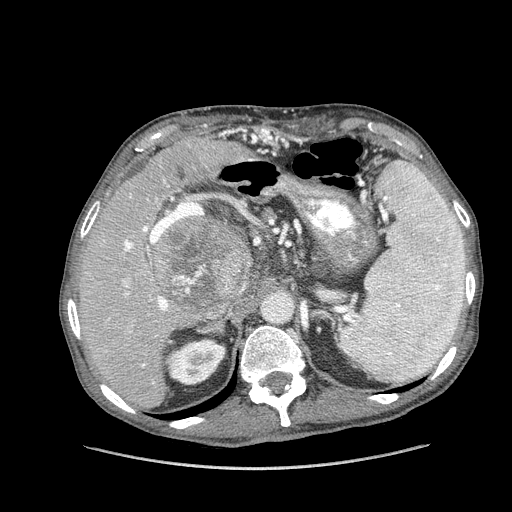
Contrast-enhanced abdominal CT (liver protocol), one axial slice; position 91 of 162 along the scan axis; reconstruction kernel STANDARD; 100 kVp; soft-tissue window (W 400 / L 40 HU); 2.5 mm slice thickness; 512 × 512 image matrix, field of view 400 × 400 mm. Case-level facts recorded for this patient, not image findings: diagnosis: hepatocellular carcinoma (patient treated with transarterial chemoembolisation; whether this scan precedes or follows treatment is not stated here); TNM stage (as recorded): Stage-IIIA; Child-Pugh class: A.
Outlined on this slice (semi-automatically segmented with operator editing):
- liver parenchyma outside the tumour (the mass and vessels are separate outlines, so this box may not span the whole liver): box from (x=78, y=136) to (x=252, y=408) px
- mass: (x=150, y=211)–(x=251, y=313)
- liver vessels: (x=108, y=166)–(x=203, y=383)